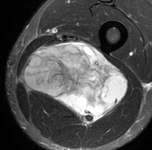
MRI of an extremity soft-tissue mass, one axial slice; STIR; MR volume resampled by the dataset authors to the PET/CT grid (not the native acquisition matrix); 3.27 mm slice thickness; 152 × 150 image matrix. Male patient. From the clinical record (not read from this slice): histological type: undifferentiated pleomorphic liposarcoma; grade: high; site of the primary tumour: left thigh.
Annotated regions visible in this slice (expert contour drawn on MRI and transferred to this co-registered scan by the dataset authors):
- gross tumour volume including surrounding oedema: box from (x=23, y=43) to (x=129, y=127) px
- gross tumour volume (mass): (x=25, y=43)–(x=129, y=127)